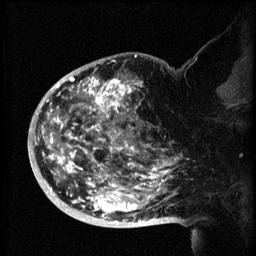
Breast MRI (dynamic contrast-enhanced), one sagittal slice; slice 39 of 60 in the series (ordered by position); 3 images stored at this slice position (order not interpretable as contrast timing); 1.5 T; TE 4.2 ms, TR 8.2 ms; 2 mm slice thickness; 256 × 256 image matrix. Female patient, age 50 years.
Annotated regions visible in this slice (semi-automatically segmented with operator editing):
- analysis volume of interest (the breast-tissue region the enhancement analysis was run in; not a lesion): box from (x=44, y=72) to (x=173, y=219) px
- tumour enhancement mask (voxels above the 70 % enhancement threshold inside the analysis volume of interest): (x=44, y=72)–(x=173, y=219)